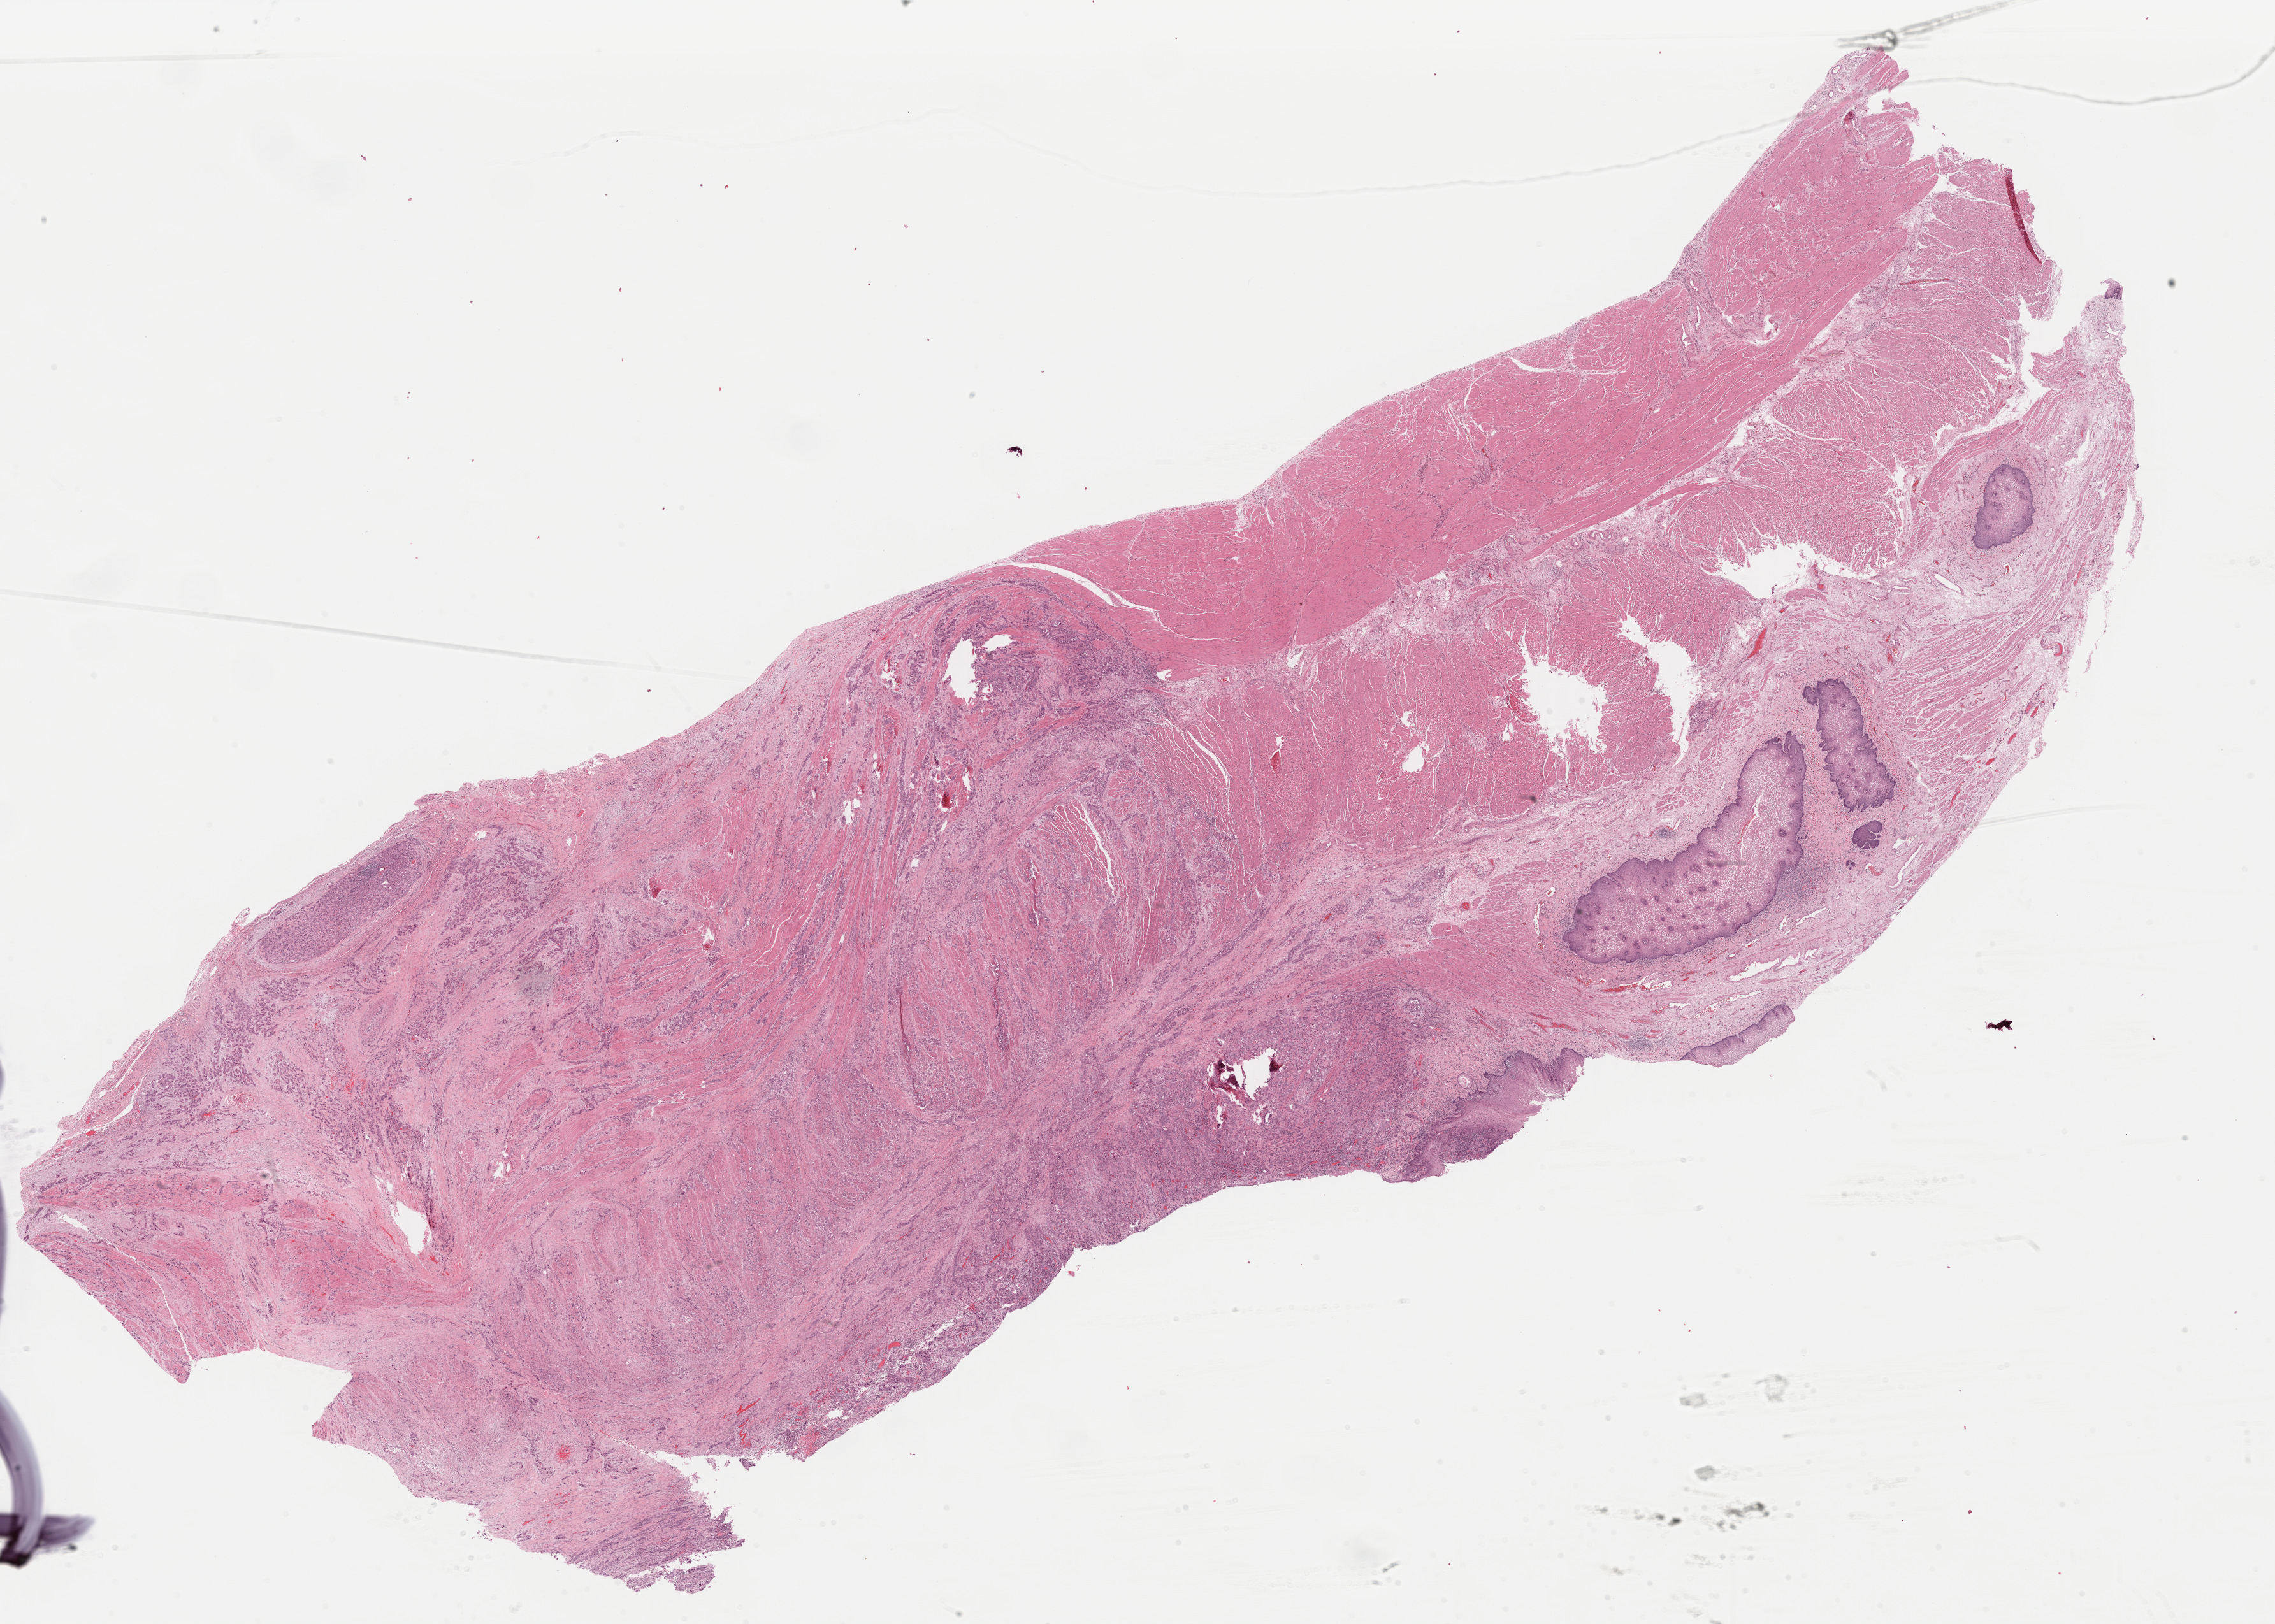
H&E whole-slide image, low-resolution overview of the scanned area, about 28.2 x 20.1 mm, formalin-fixed paraffin-embedded (FFPE) diagnostic section, esophagus, primary tumour sample. Patient sex: male. Histologic grade: G3 (poorly differentiated).
* AJCC pathologic stage: IIB
* pathologic diagnosis: Squamous cell carcinoma, NOS (middle third of esophagus)
* lymph nodes positive (case pathology): 0 of 3 examined
* TNM: T3 N0 MX